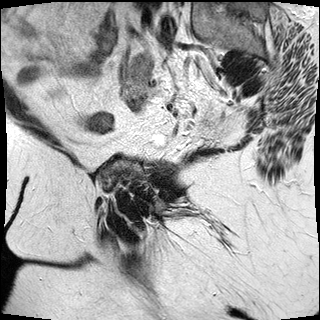
Pelvic MRI for cervical cancer, one sagittal slice. T2-weighted. 1.5 T. TE 89 ms, TR 2930 ms. 4 mm slice thickness. 320 × 320 image matrix. Patient: female, 53 years.
Structures marked on this image (manually delineated by an expert):
- uterus and cervix: bounding box (x1, y1, x2, y2) in pixels: (128, 95, 146, 113)